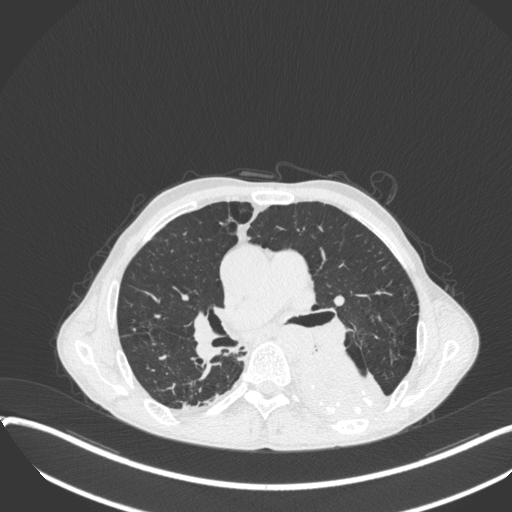
Chest CT, one axial slice. Reconstruction kernel B31f. 120 kVp. Lung window (W 1500 / L -600 HU). 512 × 512 image matrix, field of view 400 × 400 mm. Patient: male, 57 years. Case-level facts recorded for this patient, not image findings: clinical TNM (as recorded): T4 N0 M0.
Annotated regions visible in this slice (bounding box drawn by a radiologist):
- lung tumour (recorded histology: squamous cell carcinoma): bounding box (x1, y1, x2, y2) in pixels: (292, 344, 394, 427)